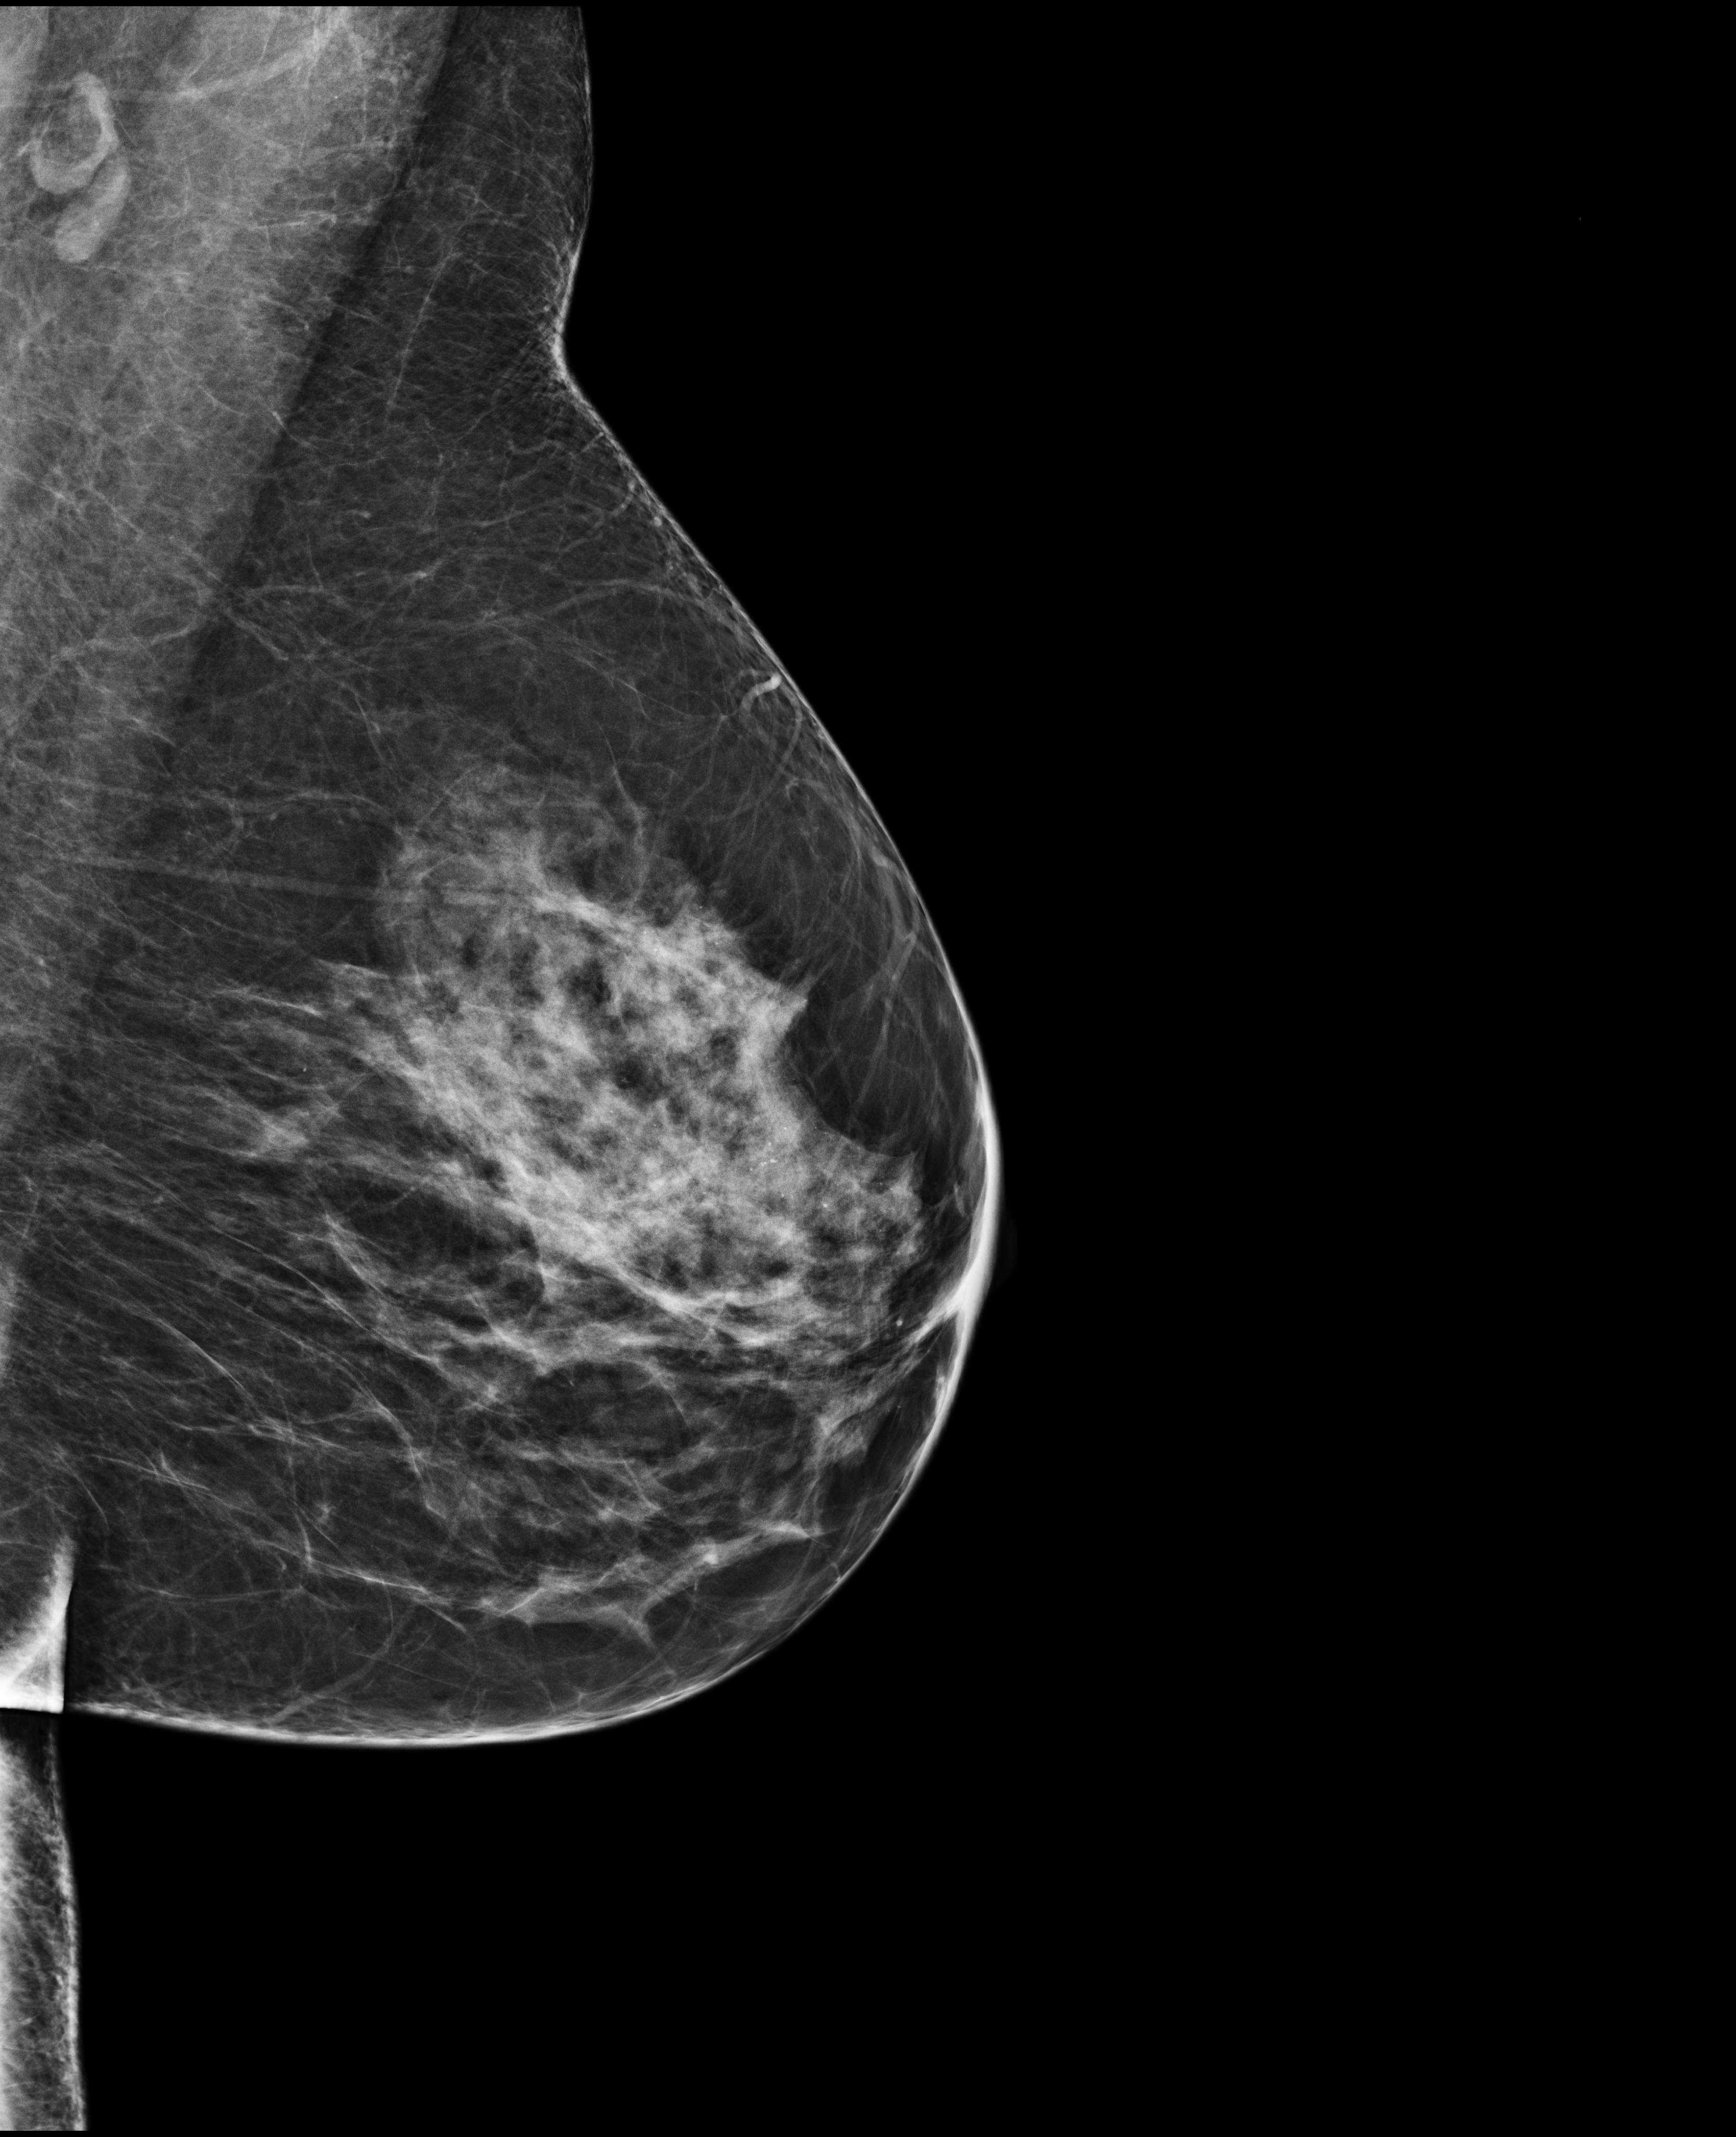
Full-field digital mammogram (FFDM), left breast, MLO view, annual screening mammography examination. Patient: female, 49 years.
BI-RADS breast density category at the screening exam (both breasts, scale 1–4): 3. Final BI-RADS assessment for this screening round (tomosynthesis exam, both breasts): category 2. Recall: no recall after this screen.